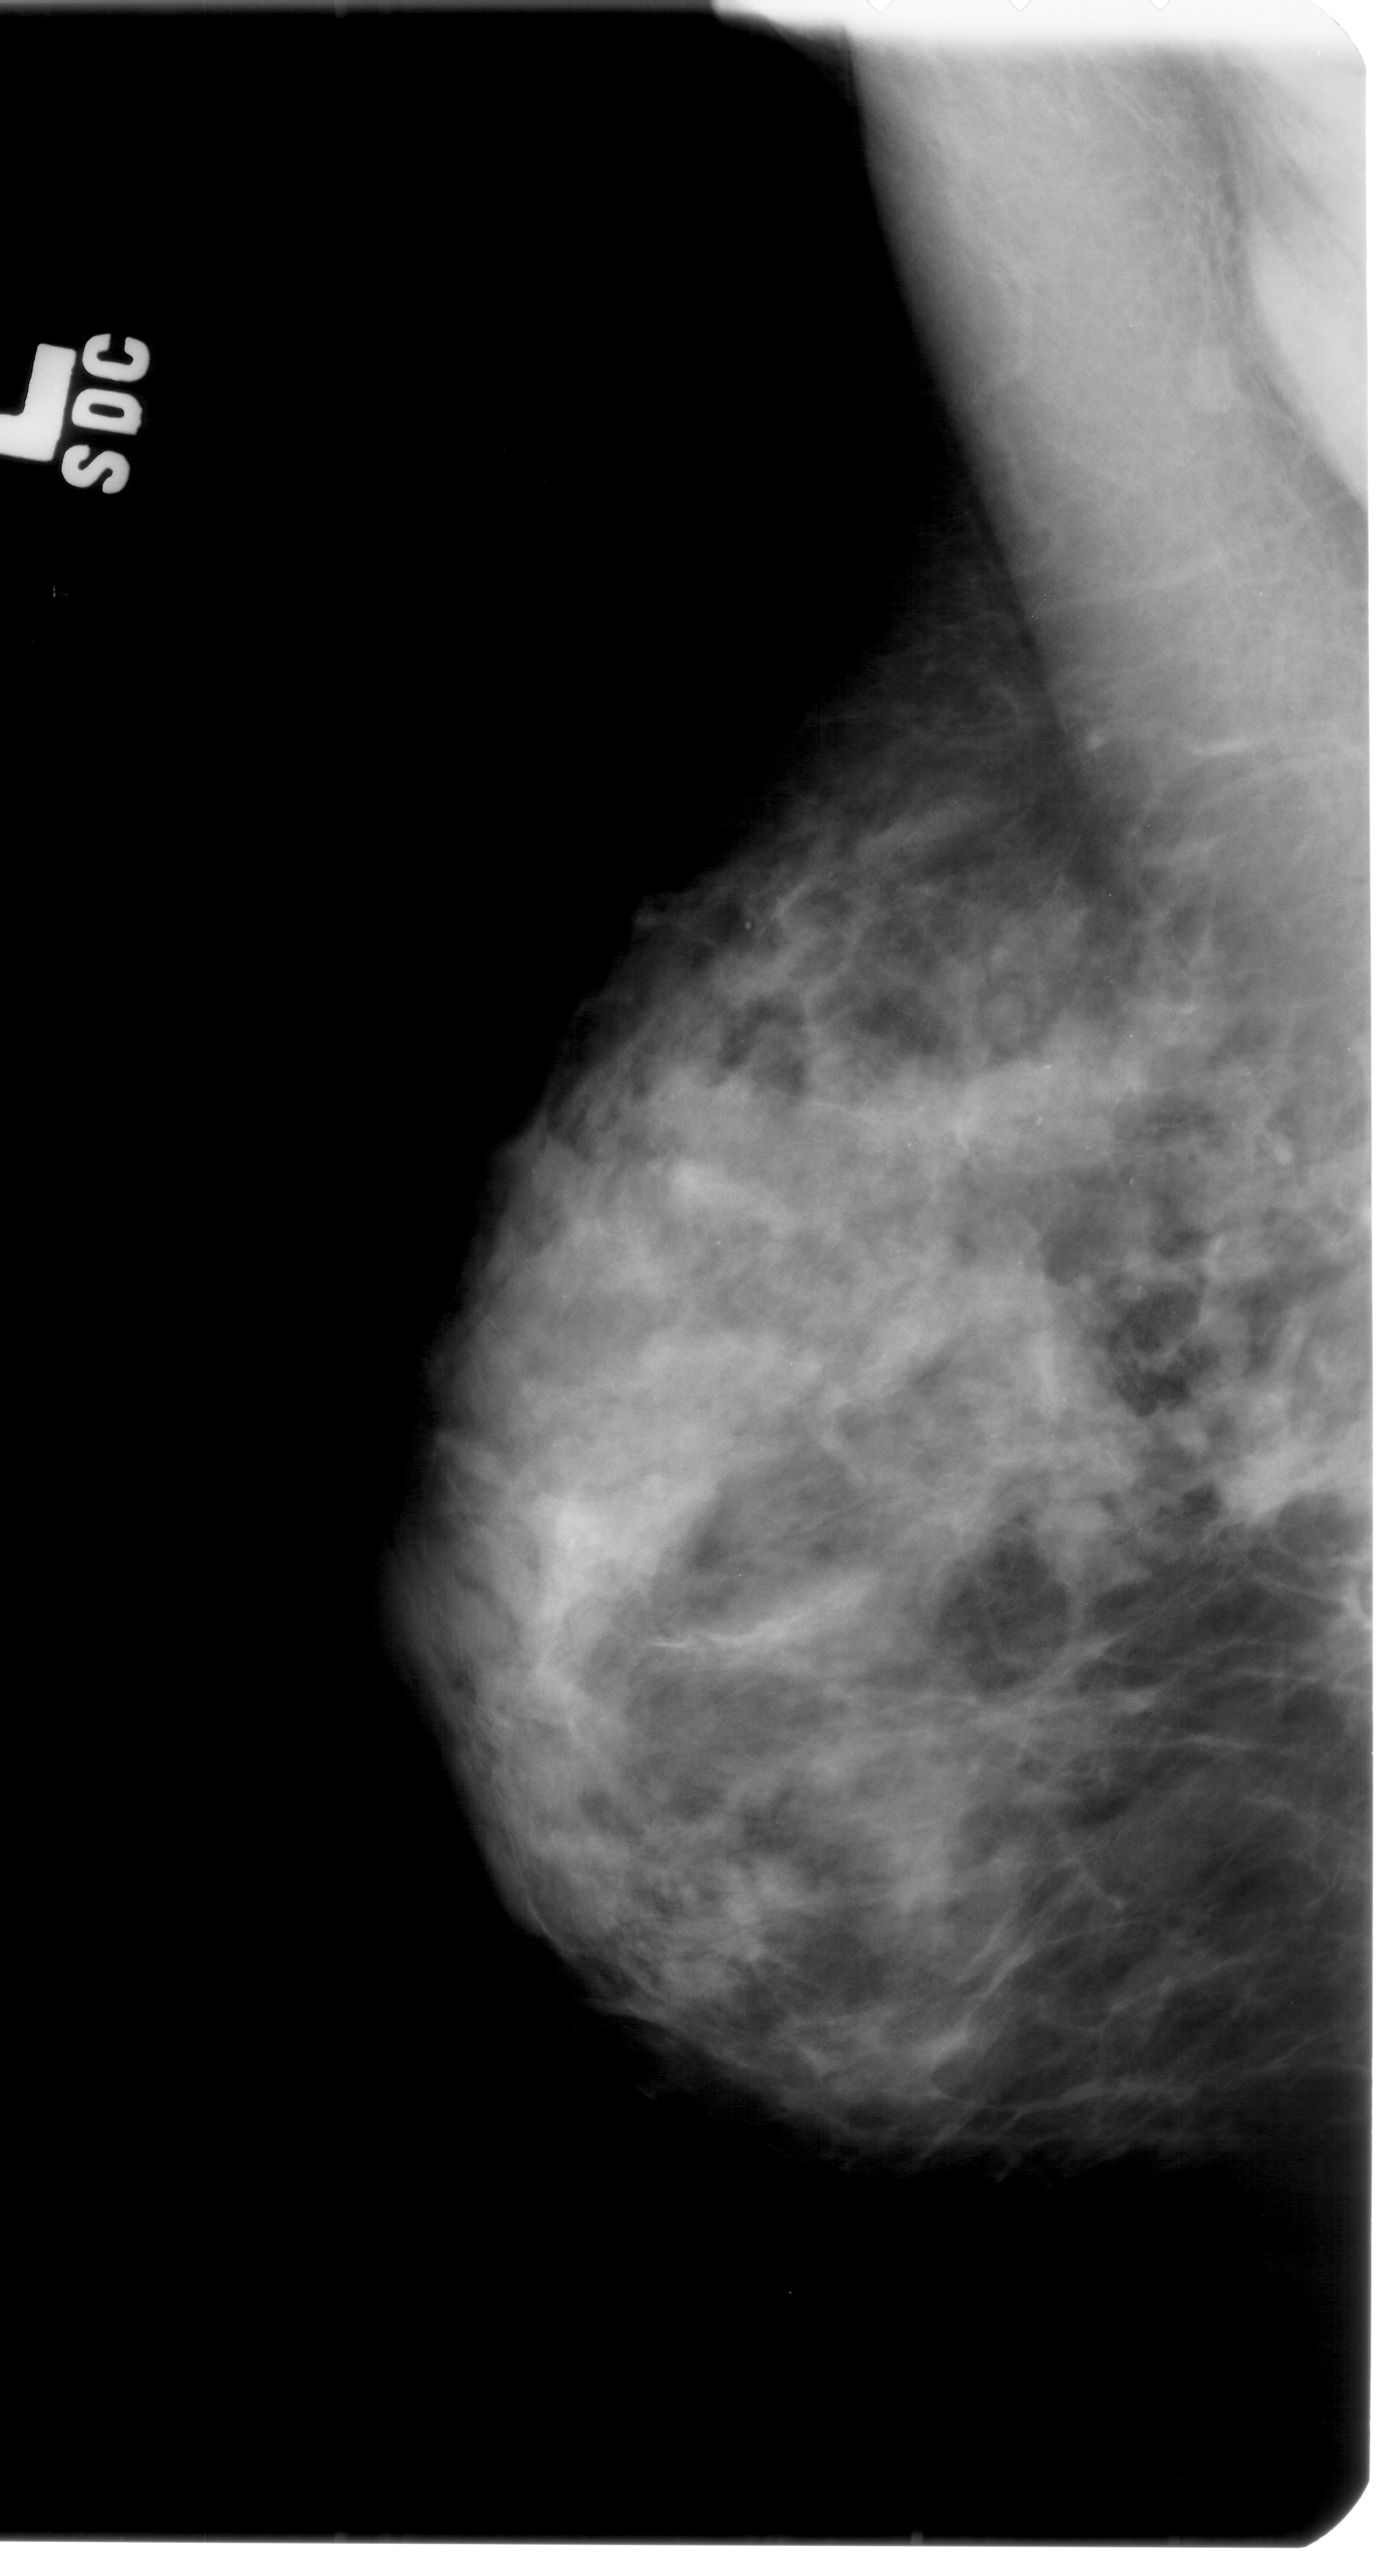
Mammogram (digitized film); left breast; MLO view; BI-RADS breast density category 3 (scale 1–4).
Marked abnormality: calcifications, morphology pleomorphic, distribution segmental; BI-RADS assessment category 4; subtlety rating 3 on a 1 (subtle) to 5 (obvious) scale; pathology (as recorded): malignant.